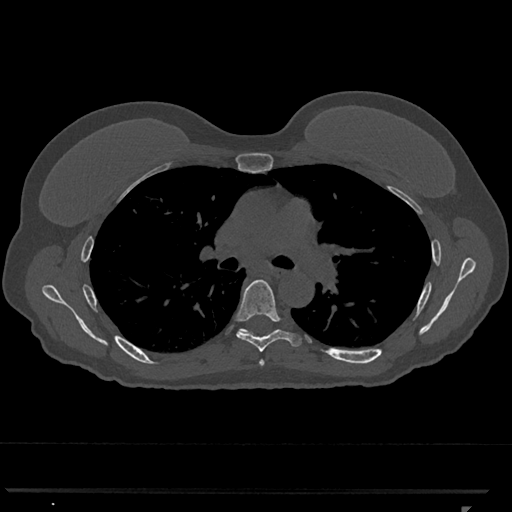
CT including the spine, one axial slice. Position 758 of 793 along the scan axis. Reconstruction kernel Br40s/3. 120 kVp. Bone window (W 1800 / L 400 HU). 512 × 512 image matrix, field of view 380 × 380 mm. Patient: female, 62 years. From the clinical record (not read from this slice): primary cancer: renal.
Structures marked on this image (semi-automatic segmentation, software-assisted and operator-edited):
- T5 vertebra: bounding box (x1, y1, x2, y2) in pixels: (259, 360, 265, 366)
- T6 vertebra: (235, 279, 301, 352)